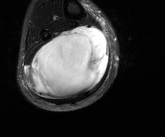
MRI of an extremity soft-tissue mass, one axial slice; slice 57 of 81 in the series (ordered by position); T2-weighted fat-saturated; MR volume resampled by the dataset authors to the PET/CT grid (not the native acquisition matrix); 3.27 mm slice thickness; 165 × 137 image matrix, field of view 161 × 134 mm. Male patient. Case-level facts recorded for this patient, not image findings: histological type: liposarcoma - round cell; grade: high; site of the primary tumour: right calf.
Outlined on this slice (expert contour drawn on MRI and transferred to this co-registered scan by the dataset authors):
- gross tumour volume (mass): bounding box <25,25,109,99> (left, top, right, bottom; pixels)